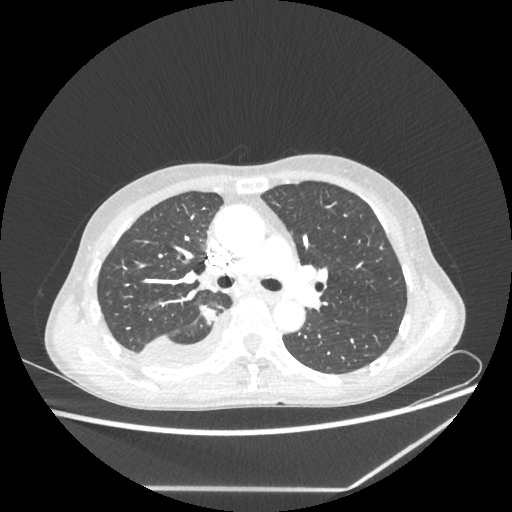
Chest CT, one axial slice; position 145 of 237 along the scan axis; lung window (W 1500 / L -600 HU); 512 × 512 image matrix, field of view 364 × 364 mm. Patient: female, 59 years. Case-level facts recorded for this patient, not image findings: clinical TNM (as recorded): T1c N1 M1.
Outlined on this slice (rectangle marked by the reading radiologist):
- lung tumour (recorded histology: adenocarcinoma): box from (x=198, y=304) to (x=217, y=327) px